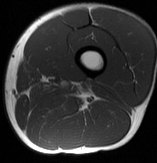
MRI of an extremity soft-tissue mass, one axial slice; position 13 of 70 along the scan axis; MR volume resampled by the dataset authors to the PET/CT grid (not the native acquisition matrix); 157 × 163 image matrix. Male patient. From the clinical record (not read from this slice): histological type: extraskeletal osteosarcoma; grade: high; site of the primary tumour: left adductur.
Annotated regions visible in this slice (expert contour drawn on MRI and transferred to this co-registered scan by the dataset authors):
- gross tumour volume (mass): box from (x=83, y=85) to (x=89, y=91) px